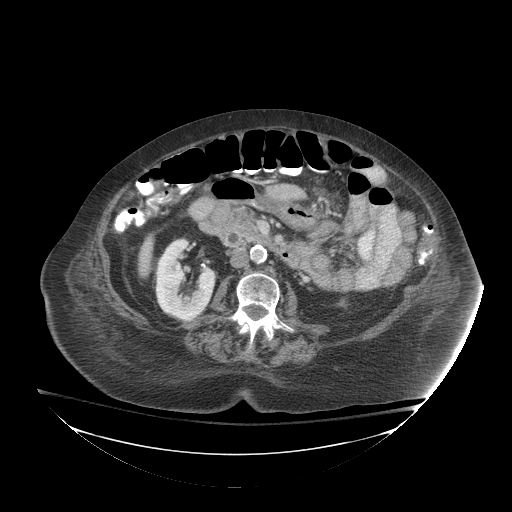
Contrast-enhanced abdominal CT (liver protocol), one axial slice. Slice 21 of 81 in the series (ordered by position). 140 kVp. Soft-tissue window (W 400 / L 40 HU). 512 × 512 image matrix, field of view 500 × 500 mm. From the clinical record (not read from this slice): diagnosis: hepatocellular carcinoma (patient treated with transarterial chemoembolisation; whether this scan precedes or follows treatment is not stated here); TNM stage (as recorded): Stage-I; Child-Pugh class: B; tumour differentiation: well-moderately differentiated; tumour nodularity: uninodular.
Annotated regions visible in this slice (semi-automatically segmented with operator editing):
- liver parenchyma outside the tumour (the mass and vessels are separate outlines, so this box may not span the whole liver): bounding box [x1, y1, x2, y2] px = [138, 236, 152, 276]